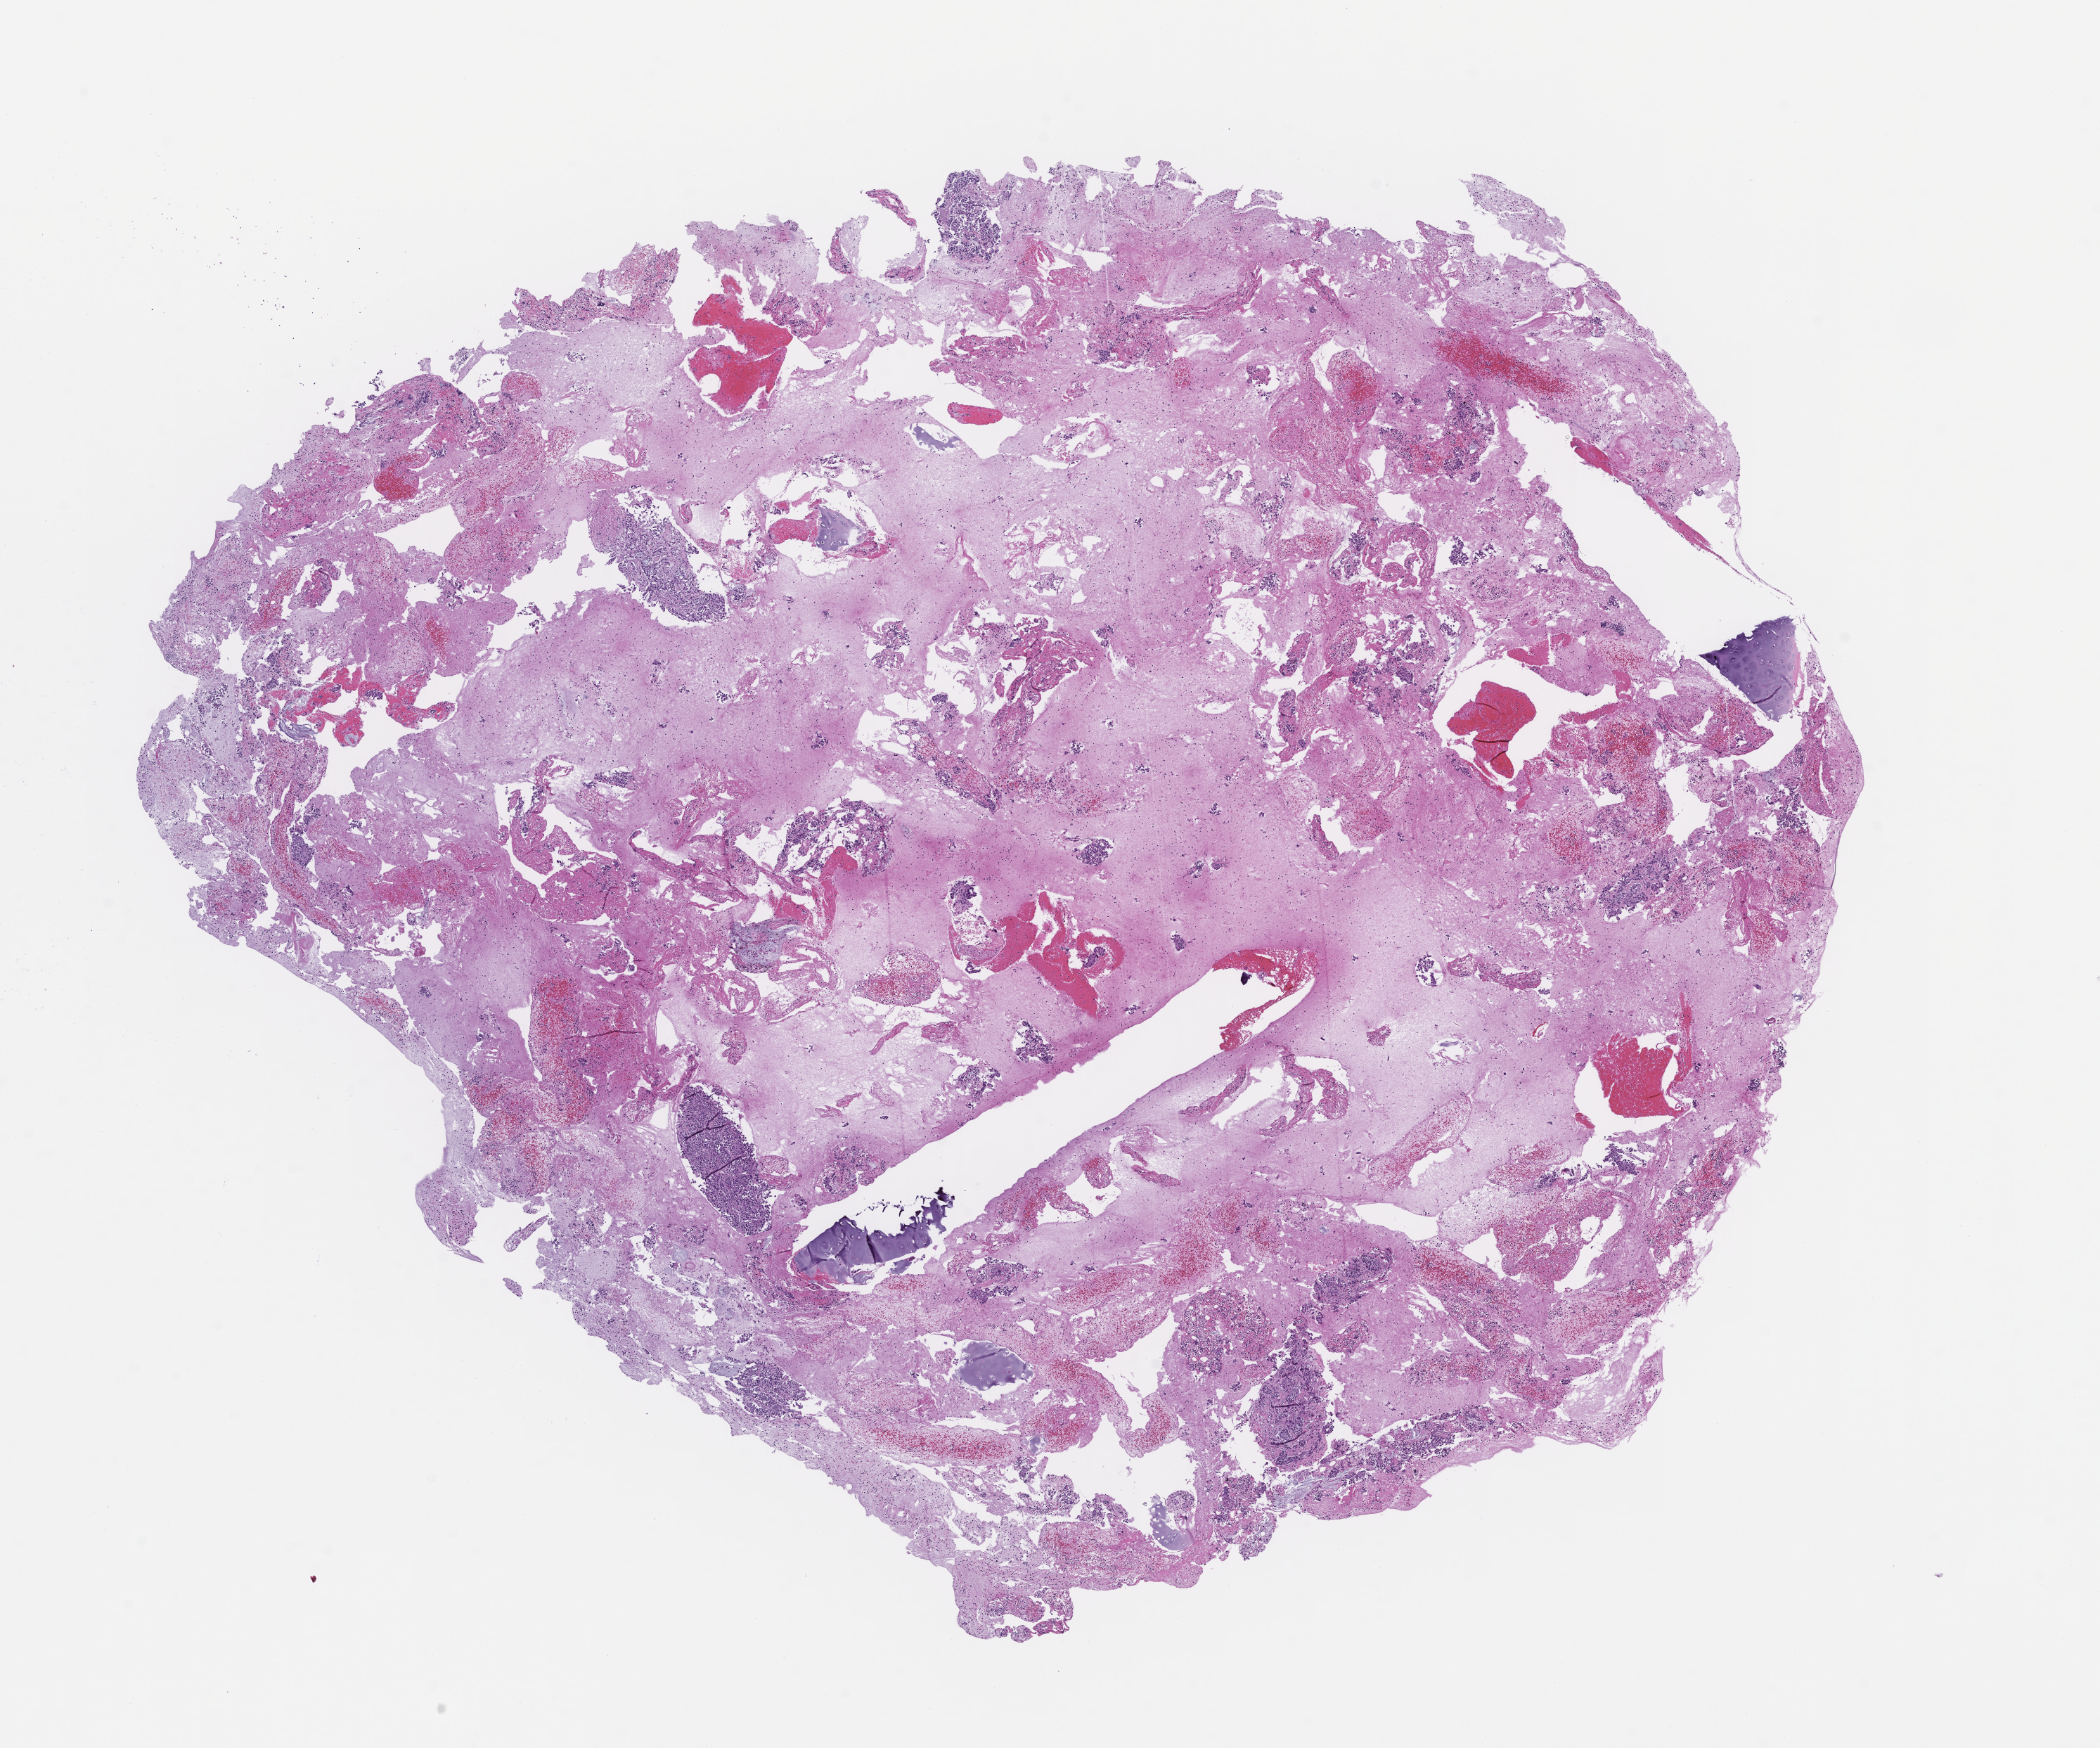
H&E whole-slide image — a low-resolution overview of the entire scanned area, about 12.1 x 10.0 mm, paraffin-embedded section, site: lung, specimen time point: collected at disease progression. Patient: male.
- this section: primary tumor
- diagnosis: Non-Small Cell Lung Carcinoma